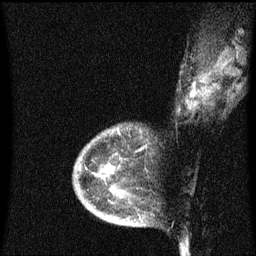
Breast MRI (dynamic contrast-enhanced), one sagittal slice; slice 23 of 60 in the series (ordered by position); dynamic contrast-enhanced series, image 2 of 3 at this slice position (ordered by acquisition); 1.5 T; TE 4.2 ms, TR 8.4 ms; 2 mm slice thickness; 256 × 256 image matrix, field of view 200 × 200 mm. Patient: female, 38 years. Case-level facts recorded for this patient, not image findings: setting: breast cancer imaged before/during neoadjuvant chemotherapy; receptor status: HR-positive, HER2-negative.
Outlined on this slice (semi-automatic segmentation, software-assisted and operator-edited):
- analysis volume of interest (the breast-tissue region the enhancement analysis was run in; not a lesion): bounding box <74,134,131,205> (left, top, right, bottom; pixels)
- tumour enhancement mask (voxels above the 70 % enhancement threshold inside the analysis volume of interest): <108,166,115,173>